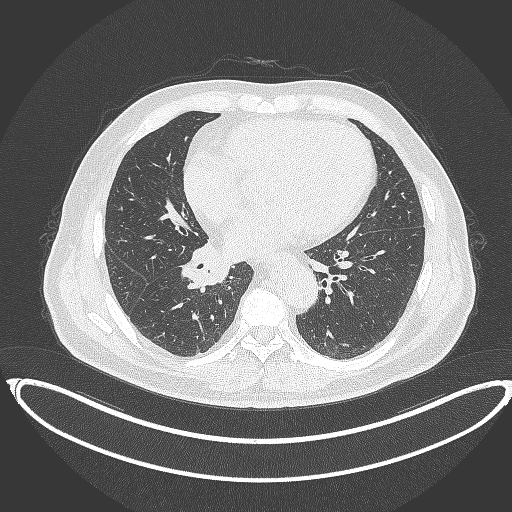
Chest CT, one axial slice; position 175 of 387 along the scan axis; 120 kVp; lung window (W 1500 / L -600 HU); 512 × 512 image matrix, field of view 448 × 448 mm. Male patient, age 61 years. Case-level facts recorded for this patient, not image findings: clinical TNM (as recorded): T1b N1 M0.
Structures marked on this image (rectangle marked by the reading radiologist):
- lung tumour (recorded histology: squamous cell carcinoma): box from (x=178, y=240) to (x=231, y=294) px